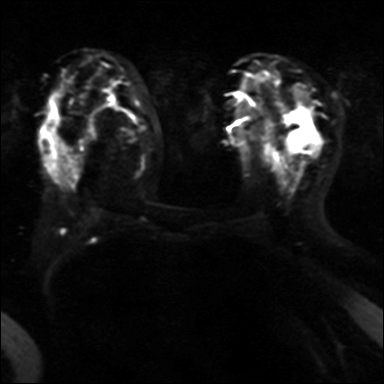
Breast MRI, one axial slice. Position 18 of 40 along the scan axis. Diffusion-weighted series; image 2 of 4 stored at this slice position (different b-values; order by instance number). 3 T. 4 mm slice thickness. 384 × 384 image matrix, field of view 320 × 320 mm. Female patient.
Annotated regions visible in this slice (manually delineated by an expert):
- tumour on diffusion-weighted imaging: bounding box (x1, y1, x2, y2) in pixels: (287, 132, 309, 149)